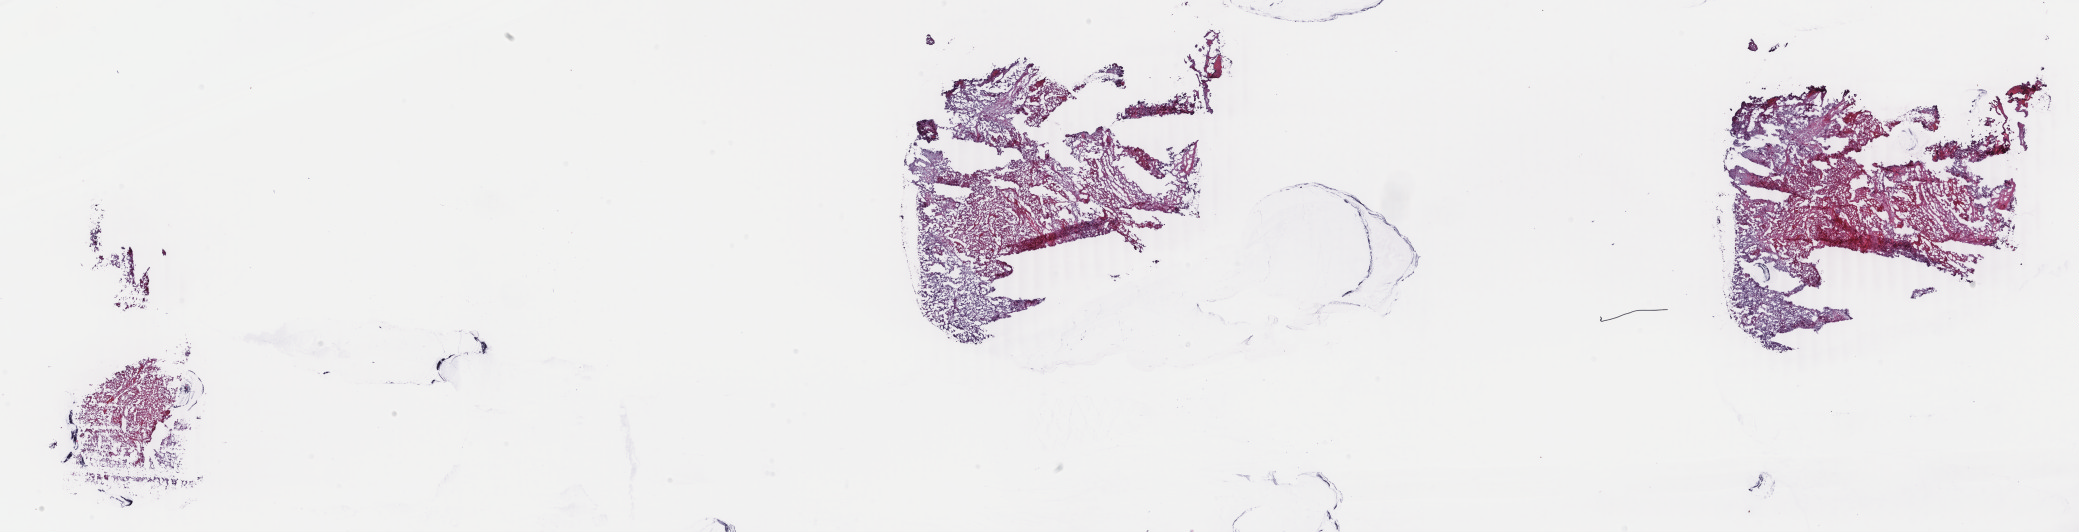
Digitized H&E tissue section (whole slide) — whole scanned area (about 33.1 x 8.5 mm, acquisition: 40x scan) shown as a low-resolution overview. Frozen section from the top of the tissue portion. Uterus, primary tumour sample. Patient: female, age at initial diagnosis 58 years. Histologic grade: G3 (poorly differentiated). Slide review estimates, as recorded: tumour cells 70%, tumour nuclei 70%, normal cells 0%, stromal cells 20%, necrosis 10%. Inflammatory infiltration, as recorded: lymphocyte infiltration 40%, monocyte infiltration 20%, neutrophil infiltration 20%.
Pathologic diagnosis: Endometrioid adenocarcinoma, NOS (endometrium). FIGO stage: IIB.